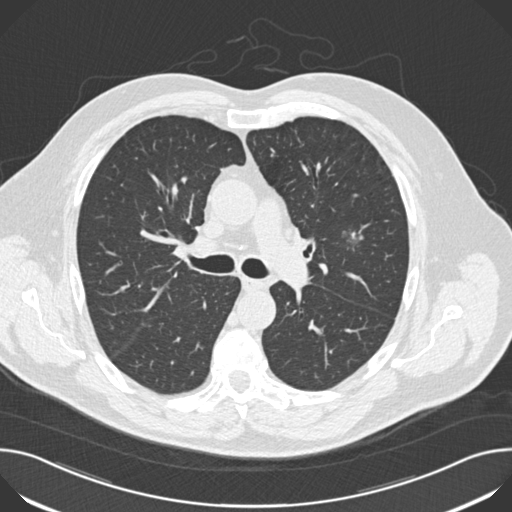
Low-dose screening chest CT, one axial slice; slice 110 of 174 in the series (ordered by position); reconstruction kernel B30f; lung window (W 1500 / L -600 HU); 2 mm slice thickness; 512 × 512 image matrix, field of view 380 × 380 mm.
Annotated regions visible in this slice (expert manual segmentation):
- lesion 1 (tumor, upper lobe of left lung): bounding box <351,231,360,239> (left, top, right, bottom; pixels)